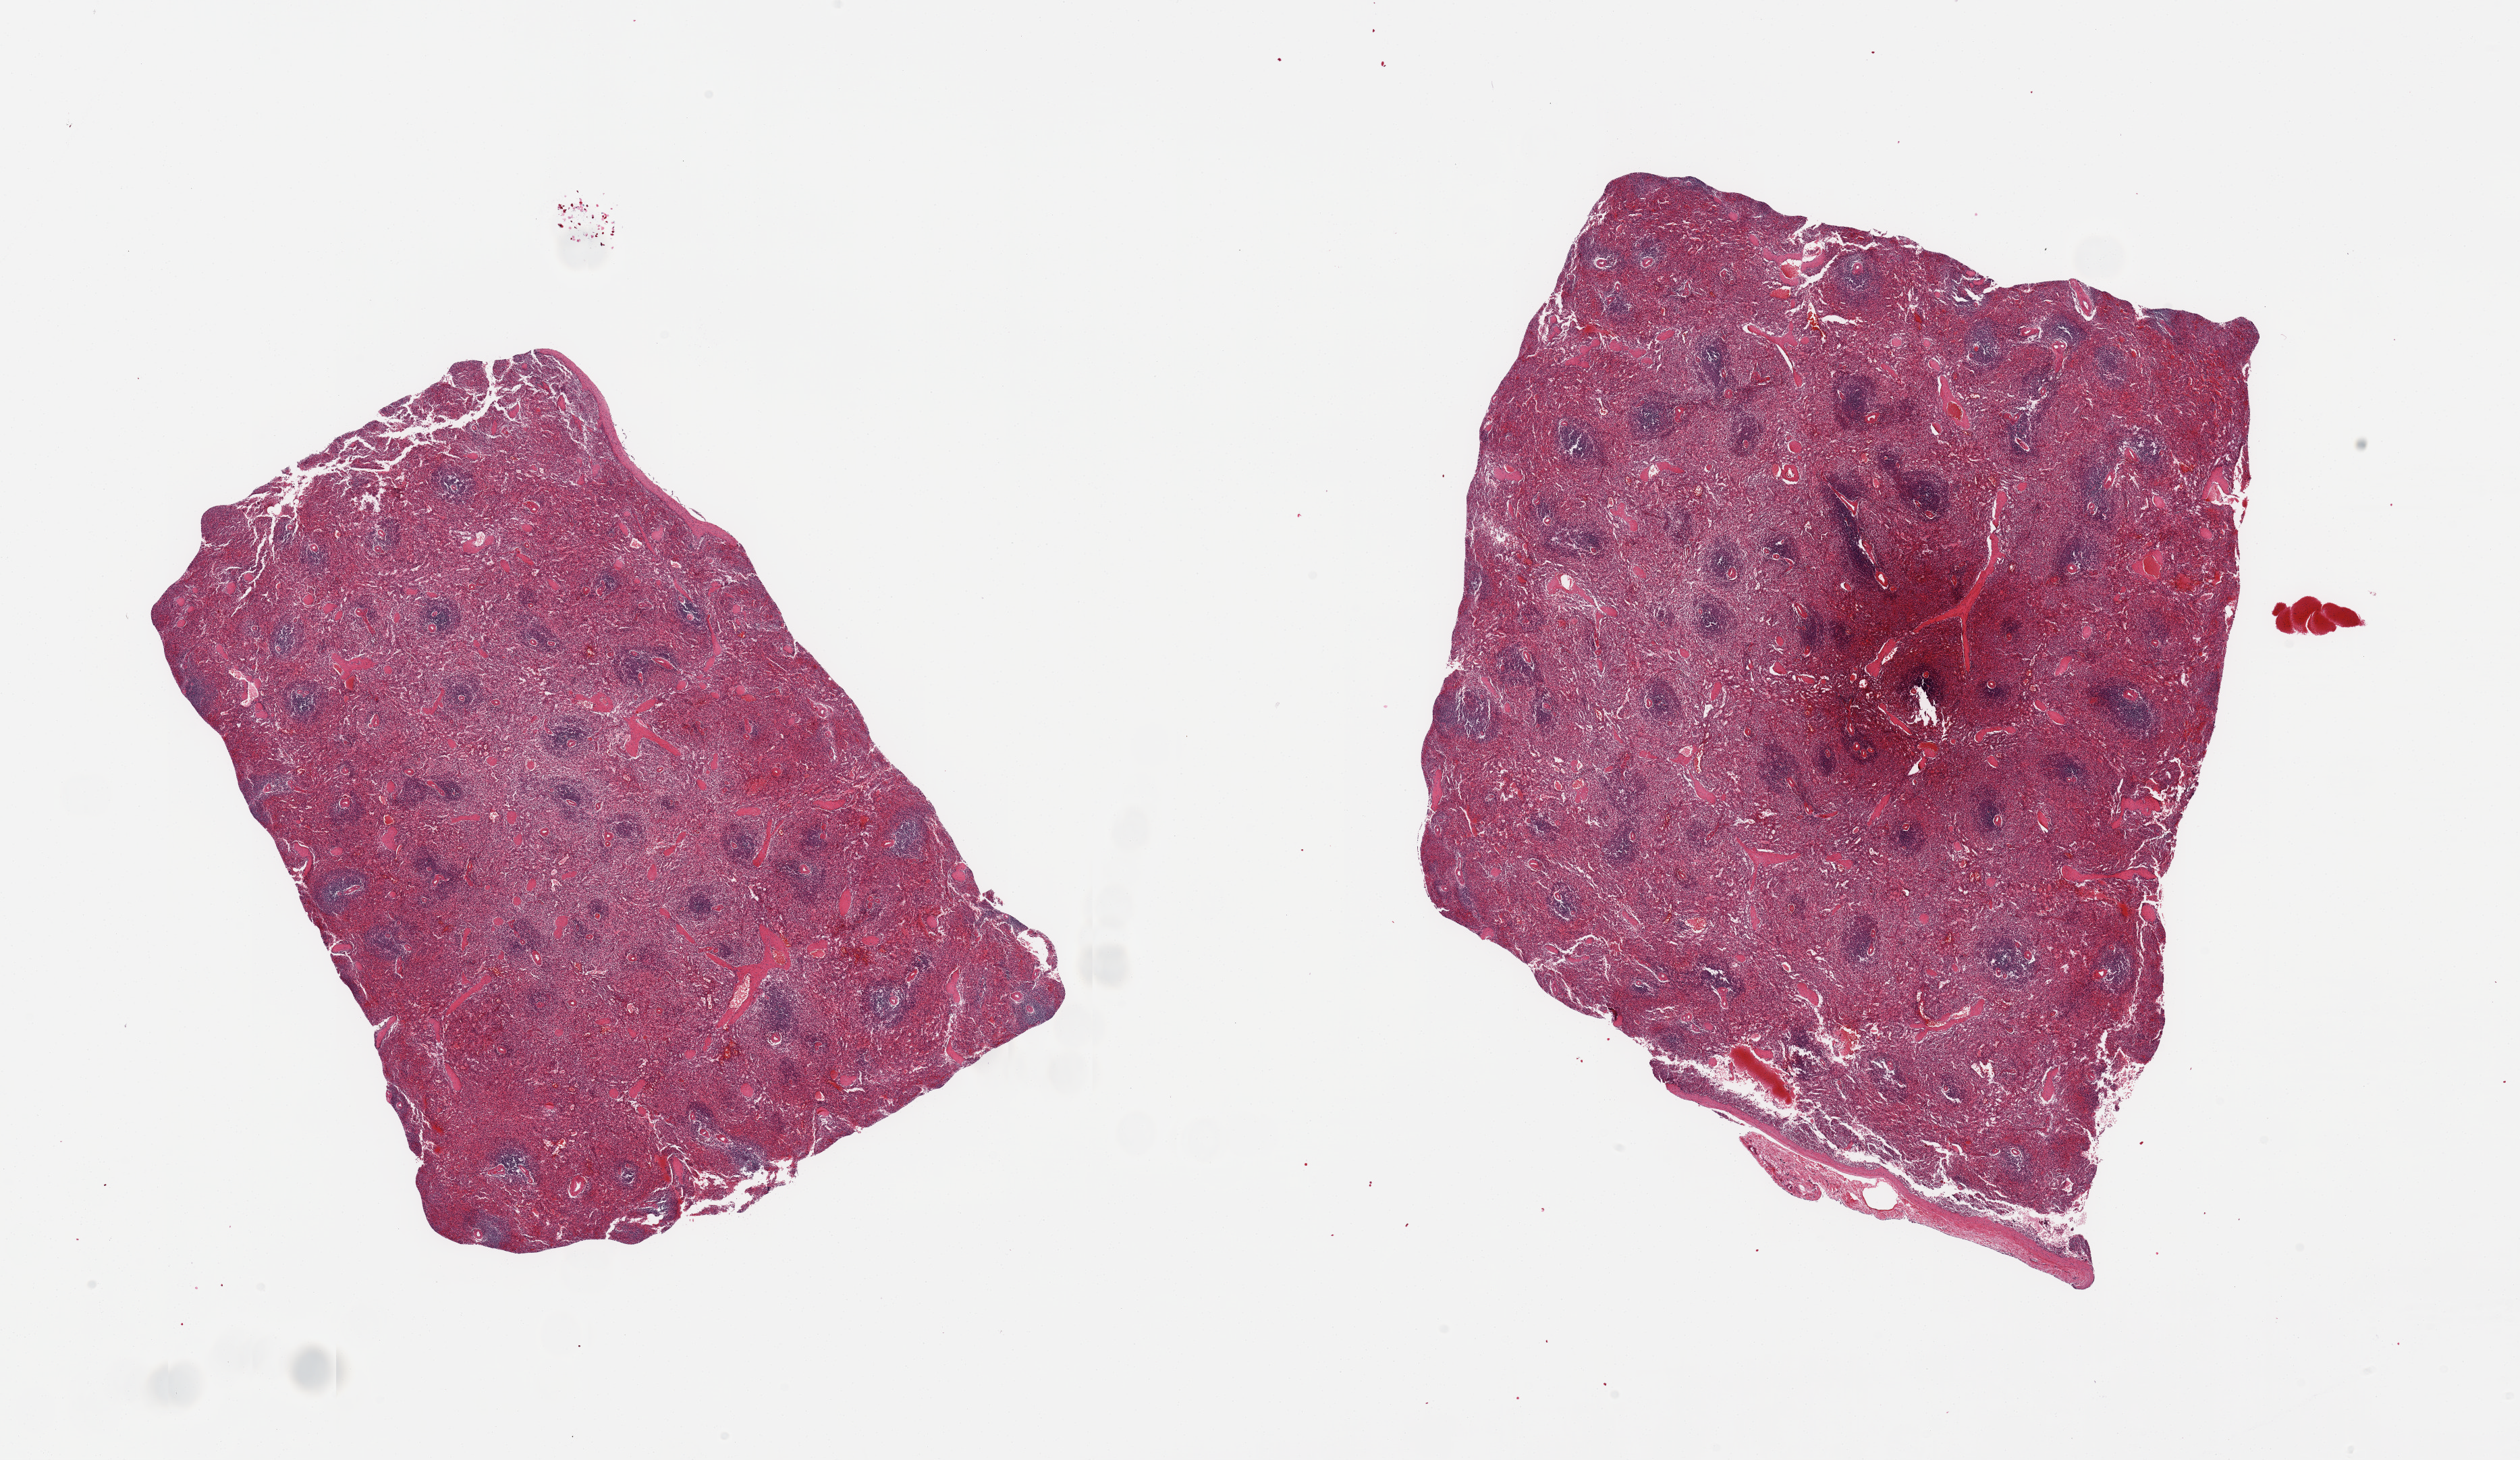
Digitized haematoxylin and eosin-stained section — shown as a low-resolution overview of the whole scanned area (about 29.5 x 17.1 mm), PAXgene-fixed paraffin-embedded (PFPE) section, sampled site (target tissue): spleen, donor tissue sample. Male donor.
Reviewer comment on this tissue sample: 2 pieces; mild congestion; small lymphoid follicles.